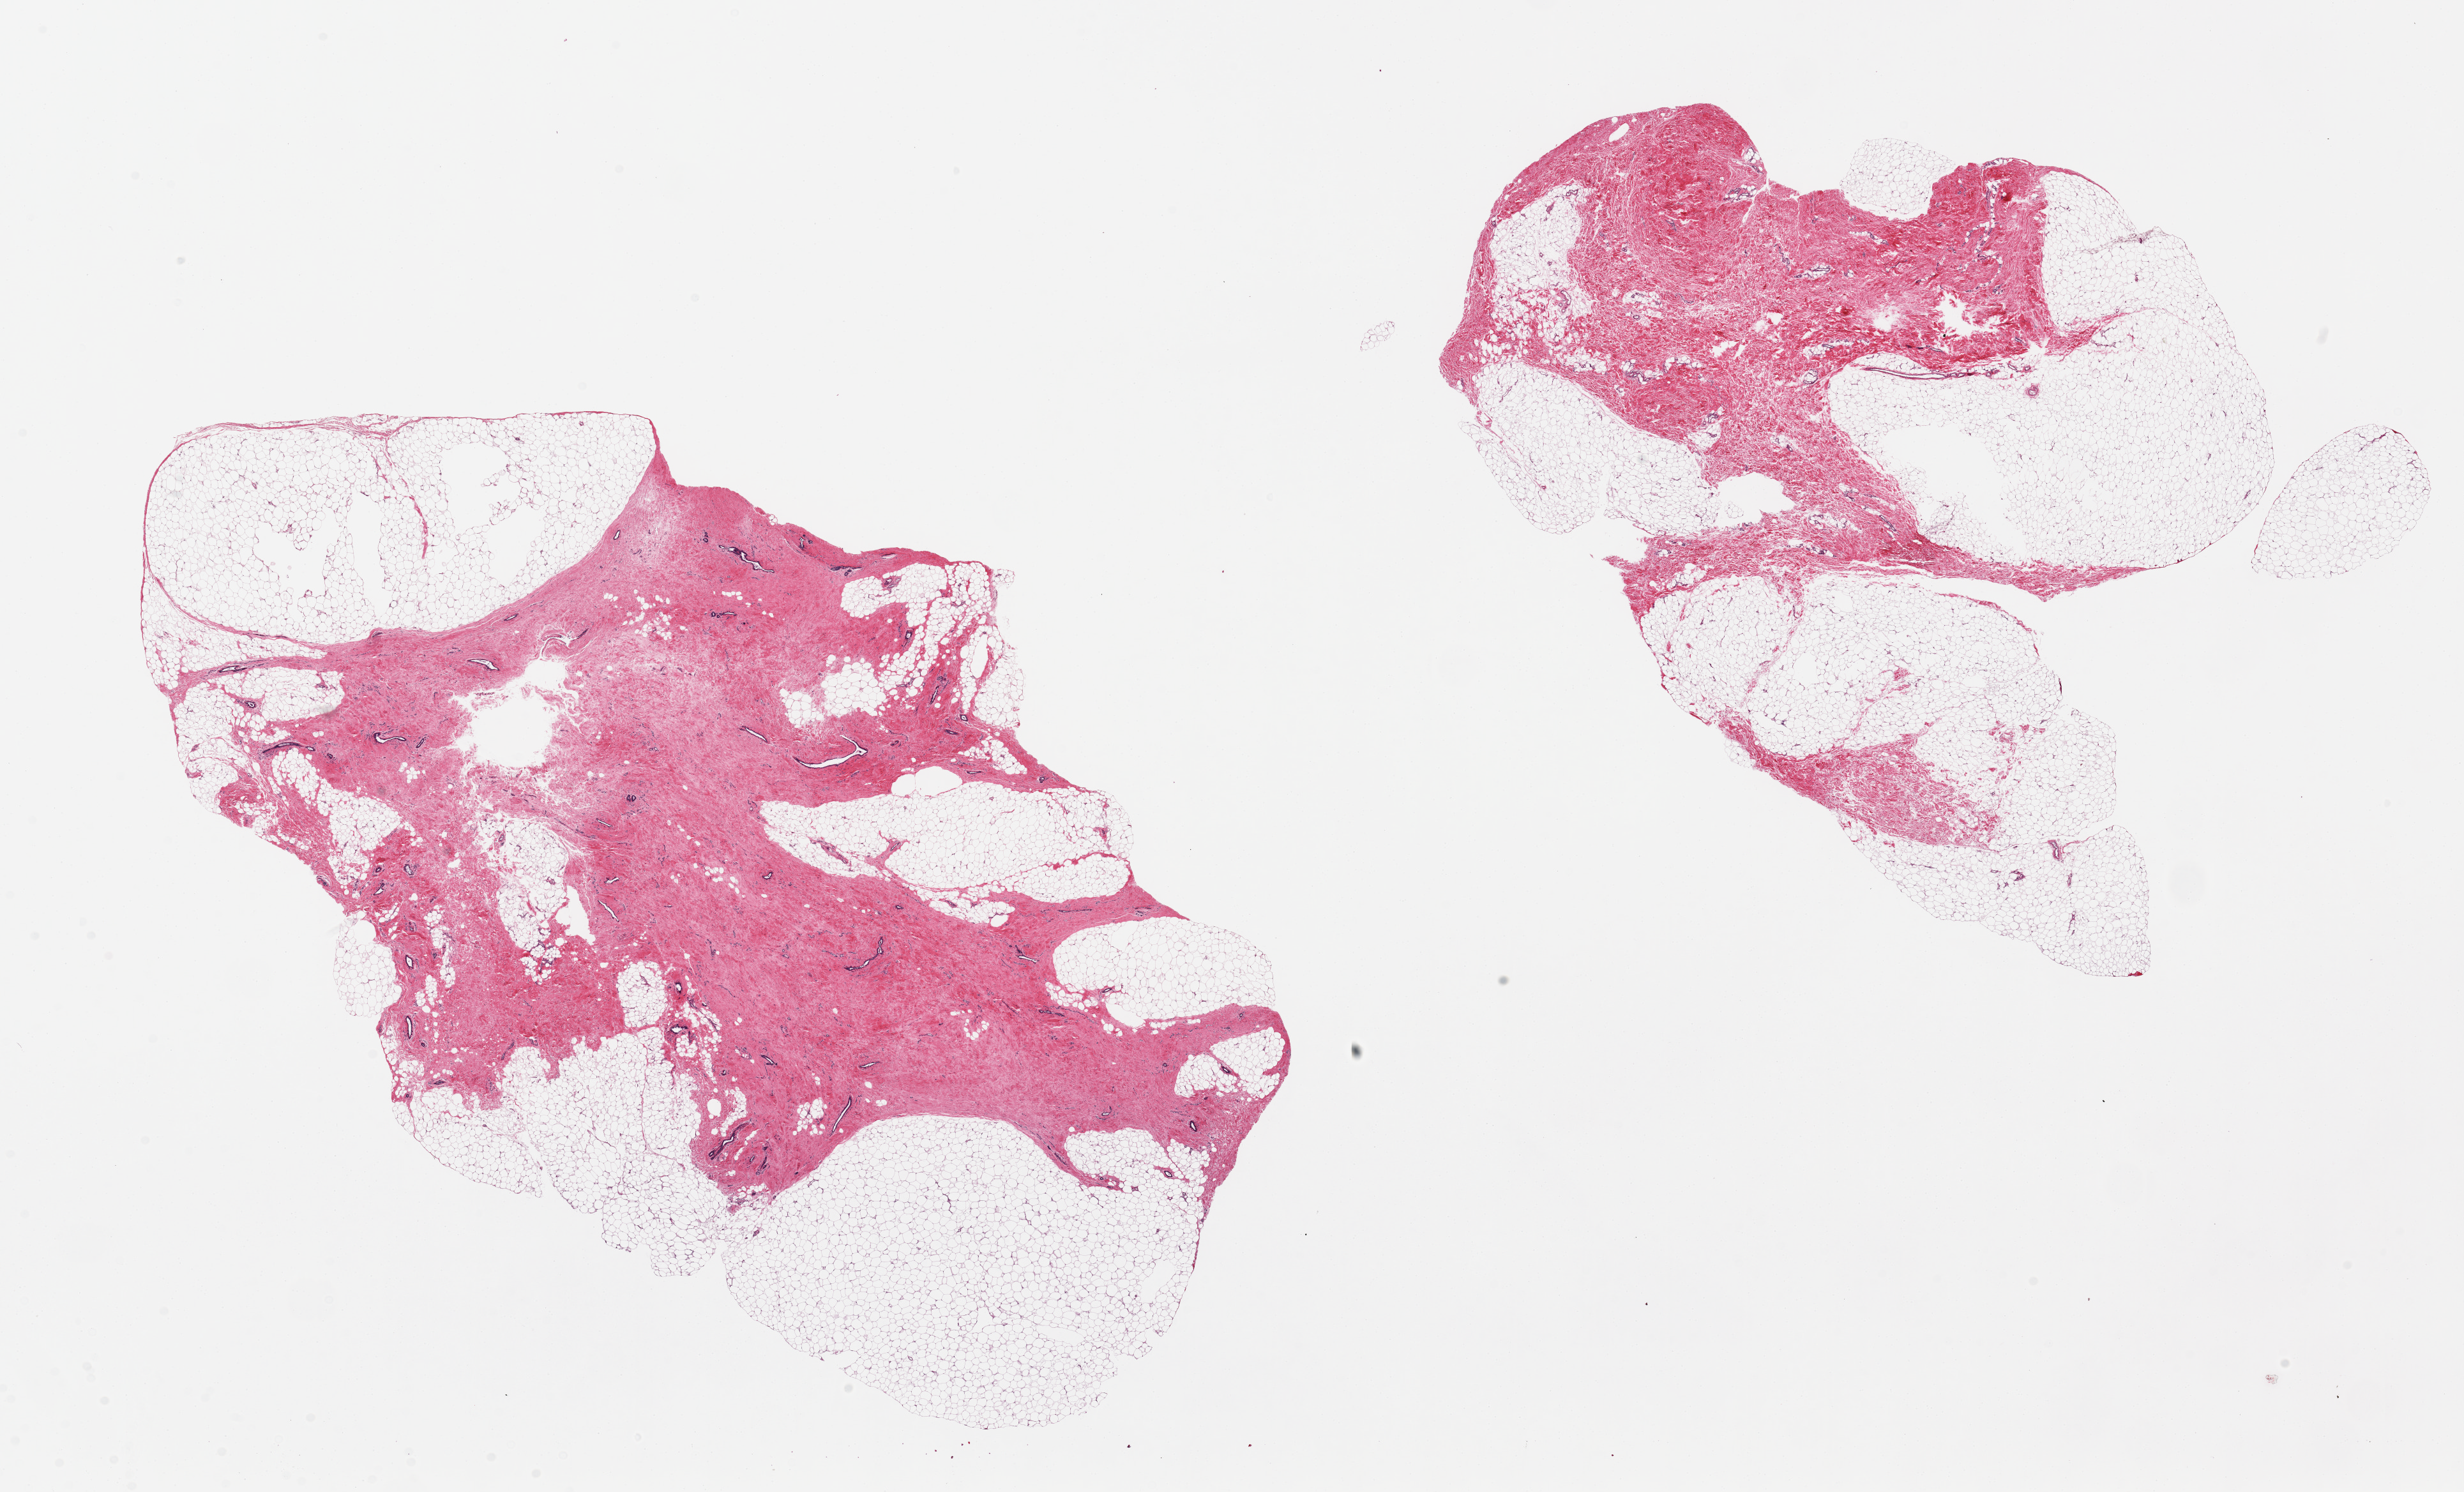
Whole-slide image, haematoxylin and eosin stain — low-resolution overview of the scanned area, about 30.5 x 18.5 mm. PAXgene-fixed, paraffin-embedded tissue. Sampled site (target tissue): breast. Donor tissue sample. Male donor.
Review note (as recorded): 2 pieces. 16.5x10 & 13x9mm. 1 with fibrous and adipose (50:50). Ducts and fibrous tissue in other with changes of gynecomastoid hyperplasia.